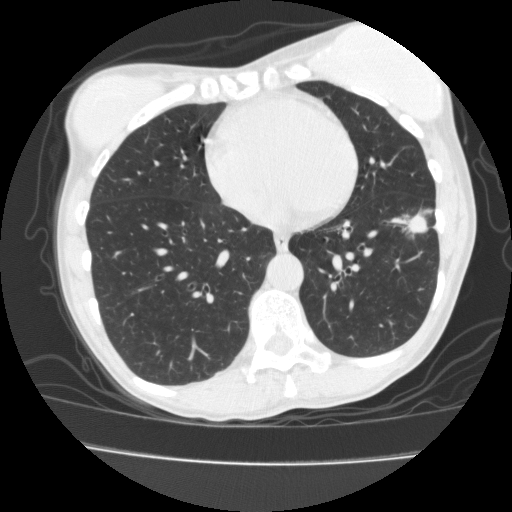
Low-dose screening chest CT, one axial slice; slice 63 of 171 in the series (ordered by position); reconstruction kernel FC10; 120 kVp; lung window (W 1500 / L -600 HU); 2 mm slice thickness; 512 × 512 image matrix, field of view 339 × 339 mm.
Structures marked on this image (expert manual segmentation):
- lesion 1 (tumor, lower lobe of left lung): bounding box [x1, y1, x2, y2] px = [406, 214, 427, 233]